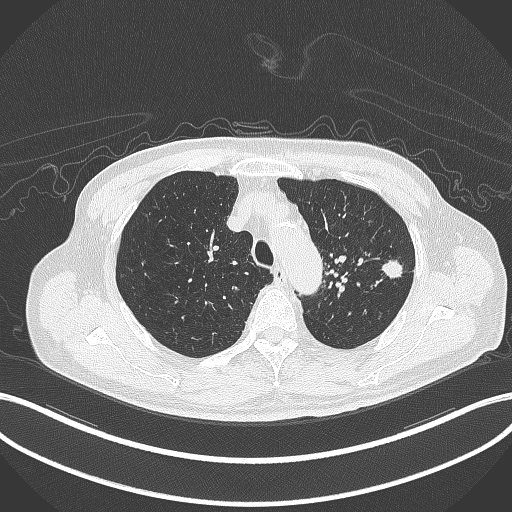
Chest CT, one axial slice; slice 344 of 417 in the series (ordered by position); 120 kVp; lung window (W 1500 / L -600 HU); 512 × 512 image matrix, field of view 400 × 400 mm. Patient: male, 77 years. From the clinical record (not read from this slice): clinical TNM (as recorded): T3 N1 M0.
Structures marked on this image (rectangle marked by the reading radiologist):
- lung tumour (recorded histology: adenocarcinoma): bounding box [x1, y1, x2, y2] px = [380, 255, 406, 283]